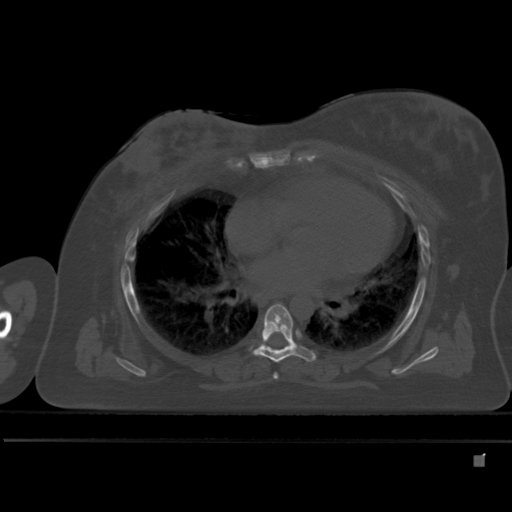
CT including the spine, one axial slice; slice 306 of 495 in the series (ordered by position); bone window (W 1800 / L 400 HU); 512 × 512 image matrix, field of view 404 × 404 mm. Female patient, age 33 years. From the clinical record (not read from this slice): primary cancer: breast; vertebrae with lytic lesions (as recorded): T1.
Structures marked on this image (semi-automatic segmentation, software-assisted and operator-edited):
- T5 vertebra: bounding box [x1, y1, x2, y2] px = [273, 373, 279, 379]
- T6 vertebra: [247, 304, 316, 363]